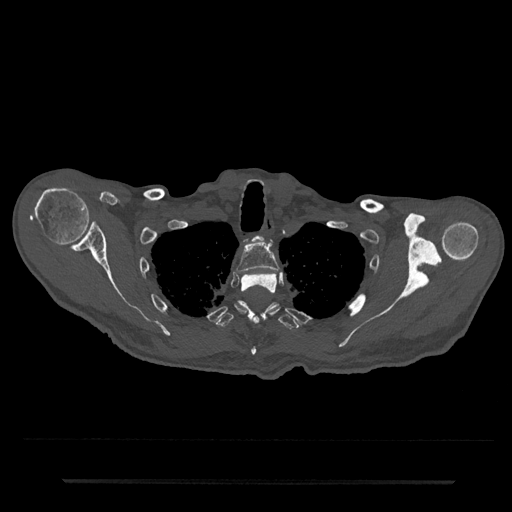
CT including the spine, one axial slice; bone window (W 1800 / L 400 HU); 0.5 mm slice thickness; 512 × 512 image matrix, field of view 427 × 427 mm. Patient: male, 74 years. From the clinical record (not read from this slice): primary cancer: prostate.
Outlined on this slice (semi-automatically segmented with operator editing):
- T1 vertebra: box from (x=258, y=236) to (x=264, y=240) px
- T2 vertebra: (x=236, y=242)–(x=279, y=273)
- T3 vertebra: (x=238, y=273)–(x=279, y=356)
- T4 vertebra: (x=216, y=300)–(x=300, y=329)